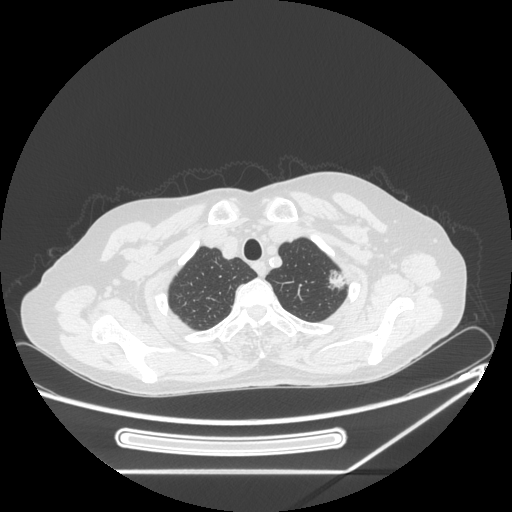
Chest CT, one axial slice. Slice 212 of 250 in the series (ordered by position). Reconstruction kernel STANDARD. 120 kVp. Lung window (W 1500 / L -600 HU). 1.25 mm slice thickness. 512 × 512 image matrix. Female patient, age 57 years. From the clinical record (not read from this slice): clinical TNM (as recorded): T1c N0 M0.
Outlined on this slice (bounding box drawn by a radiologist):
- lung tumour (recorded histology: adenocarcinoma): box from (x=323, y=268) to (x=348, y=292) px